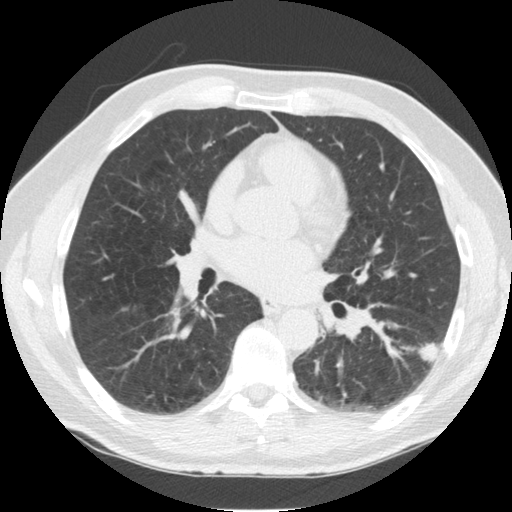
Chest CT (low-dose screening protocol), one axial image, third annual screen, lung window (W 1500 / L -600 HU), standard (soft-tissue) reconstruction kernel (STANDARD), 120 kVp, 512 × 512 image matrix. Male, age 57 years at enrolment. Former smoker at enrolment.
Lesion marked by an expert reader, bounding box (x1, y1, x2, y2) in pixels: (408, 326, 451, 373). Screening reader's record for this exam (one nodule recorded; not confirmed to be the boxed lesion): non-calcified nodule or mass ≥4 mm, left lower lobe, 13 × 12 mm, spiculated (stellate) margins, soft tissue attenuation, pre-existing on the prior screen: yes; interval growth: yes. Official screen result: positive, other.